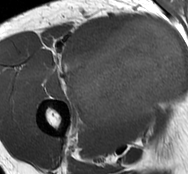
MRI of an extremity soft-tissue mass, one axial slice; slice 50 of 93 in the series (ordered by position); MR volume resampled by the dataset authors to the PET/CT grid (not the native acquisition matrix); 3.27 mm slice thickness; 188 × 174 image matrix, field of view 184 × 170 mm. Male patient. From the clinical record (not read from this slice): histological type: undifferentiated - pleiomorphic; grade: high; site of the primary tumour: right thigh.
Structures marked on this image (expert contour drawn on MRI and transferred to this co-registered scan by the dataset authors):
- gross tumour volume including surrounding oedema: box from (x=70, y=19) to (x=185, y=130) px
- gross tumour volume (mass): (x=74, y=19)–(x=185, y=129)